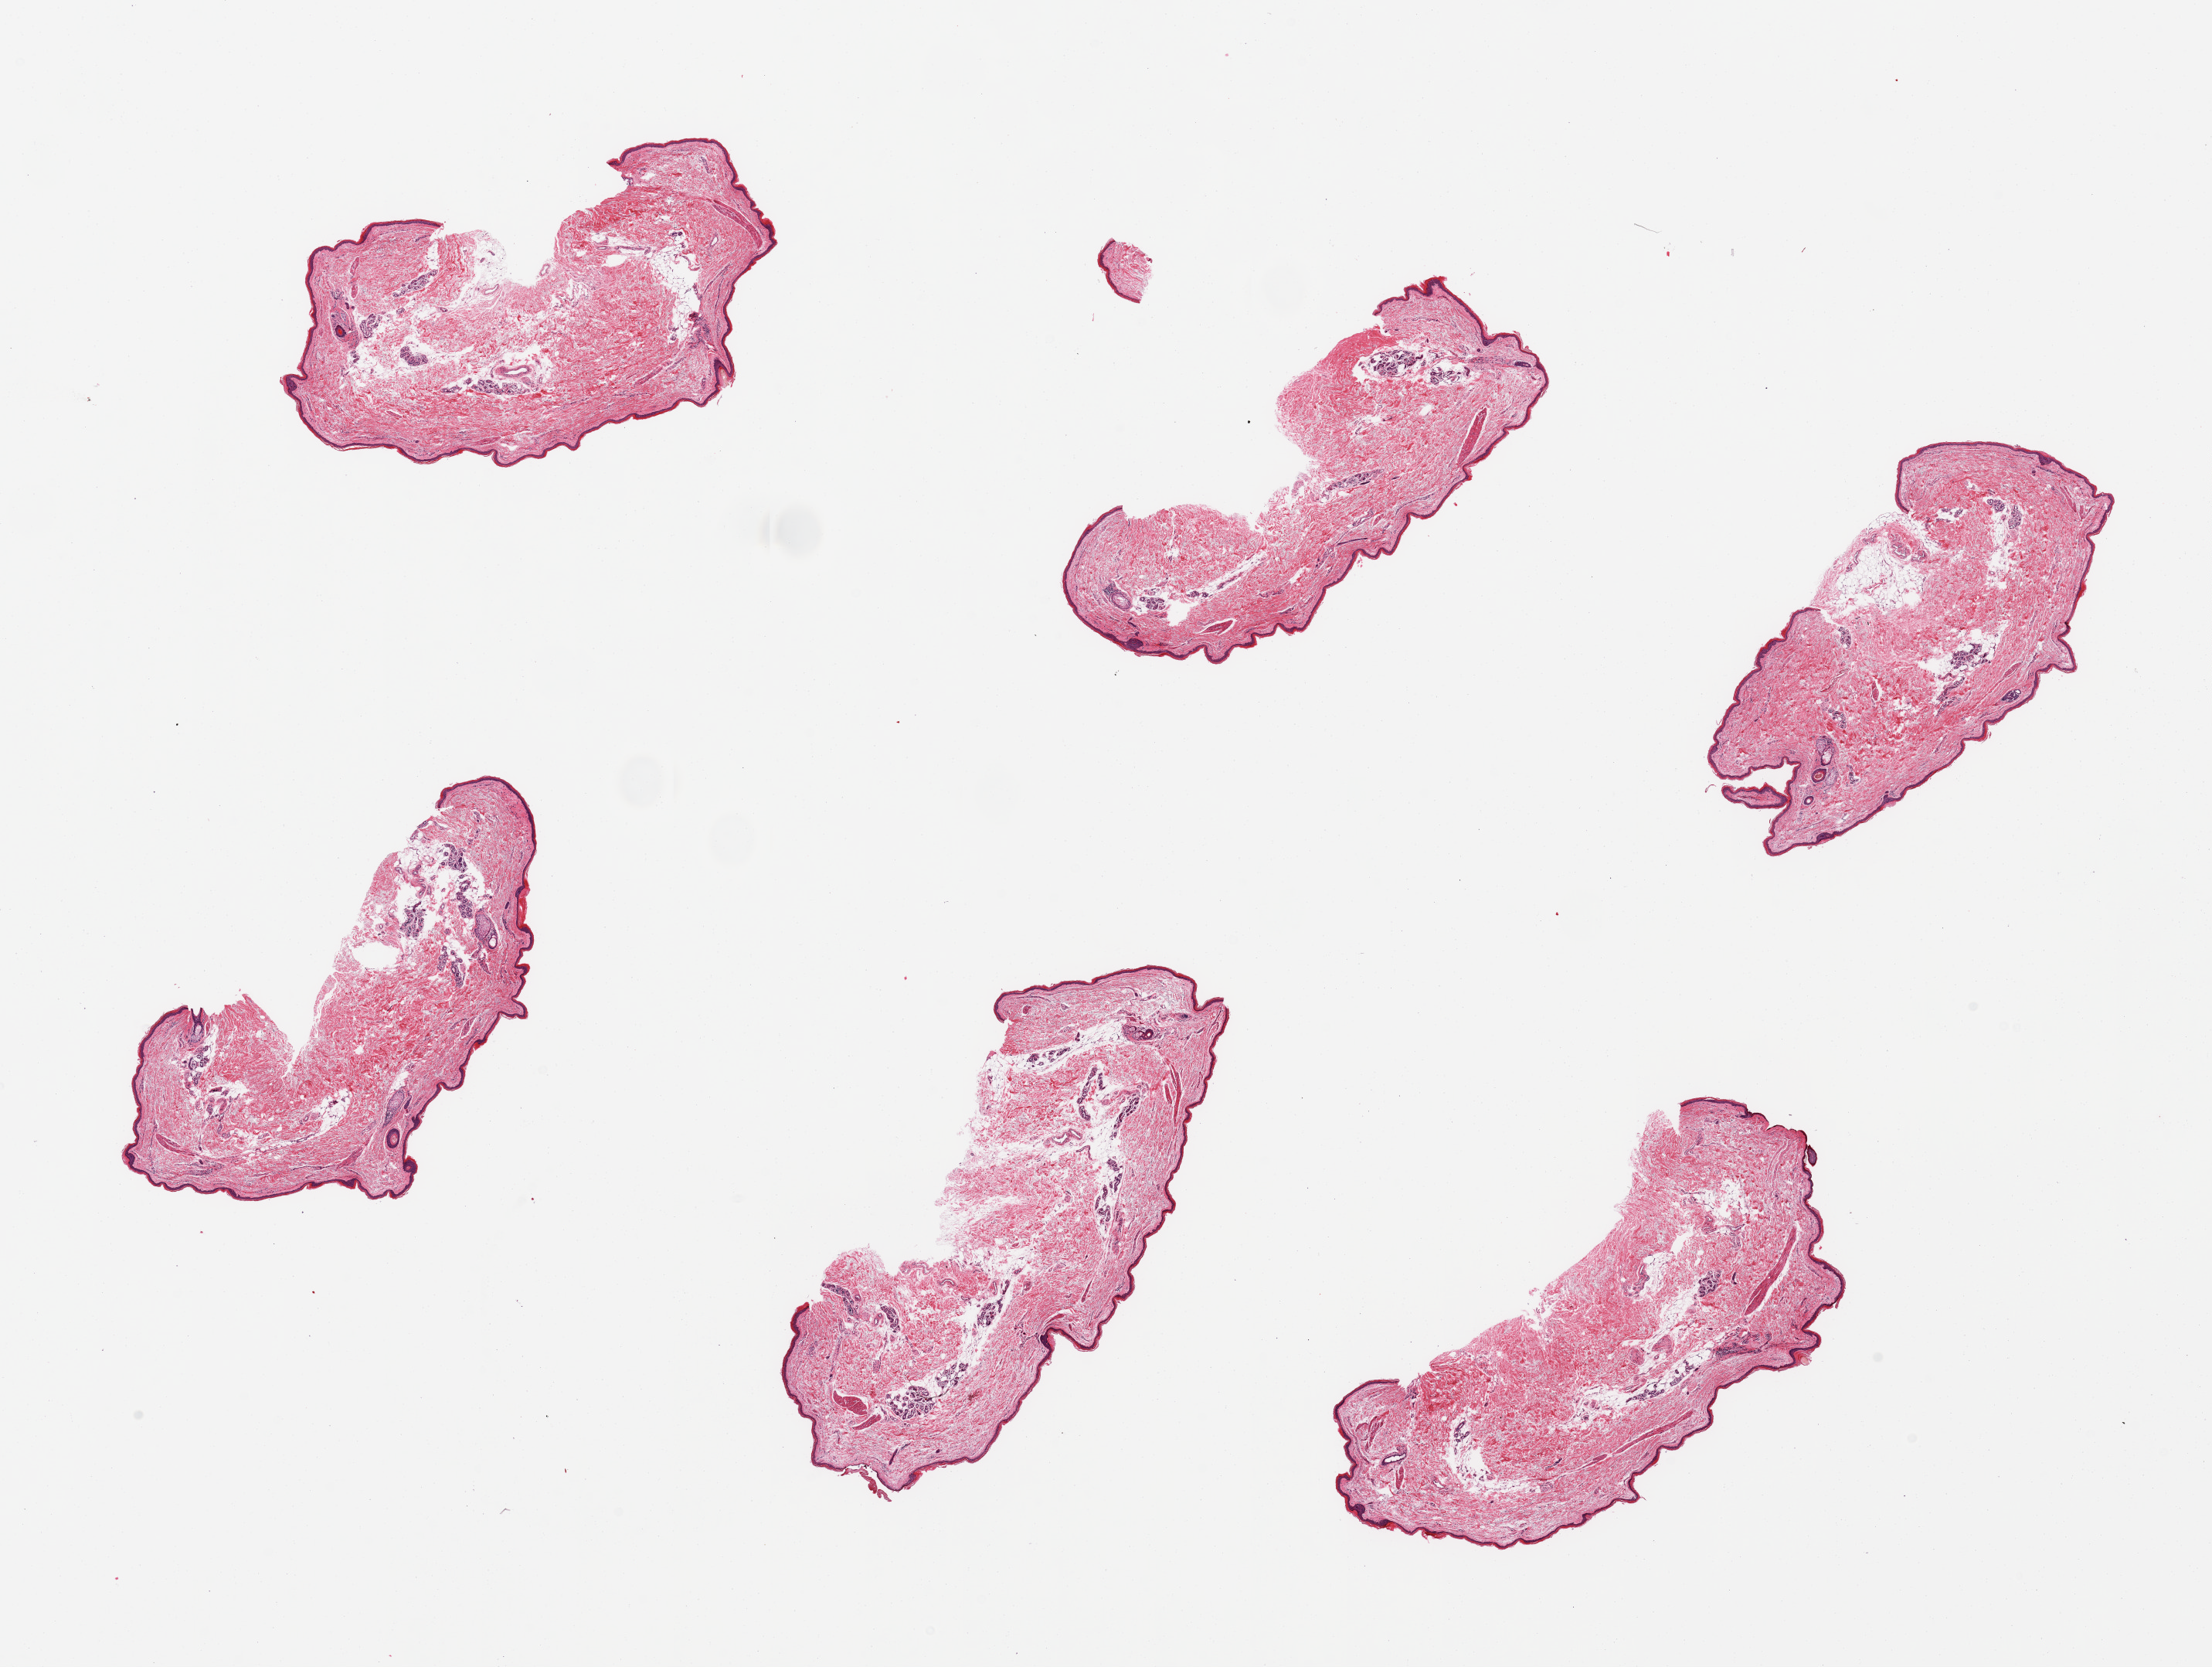
Whole-slide image, H&E stain, whole scanned area (about 22.6 x 17.1 mm, slide scanned at 20x) shown as a low-resolution overview, PAXgene-fixed, paraffin-embedded tissue, target tissue: skin of lower leg, tissue donor sample.
Review note (as recorded): 6 pieces; well trimmed.